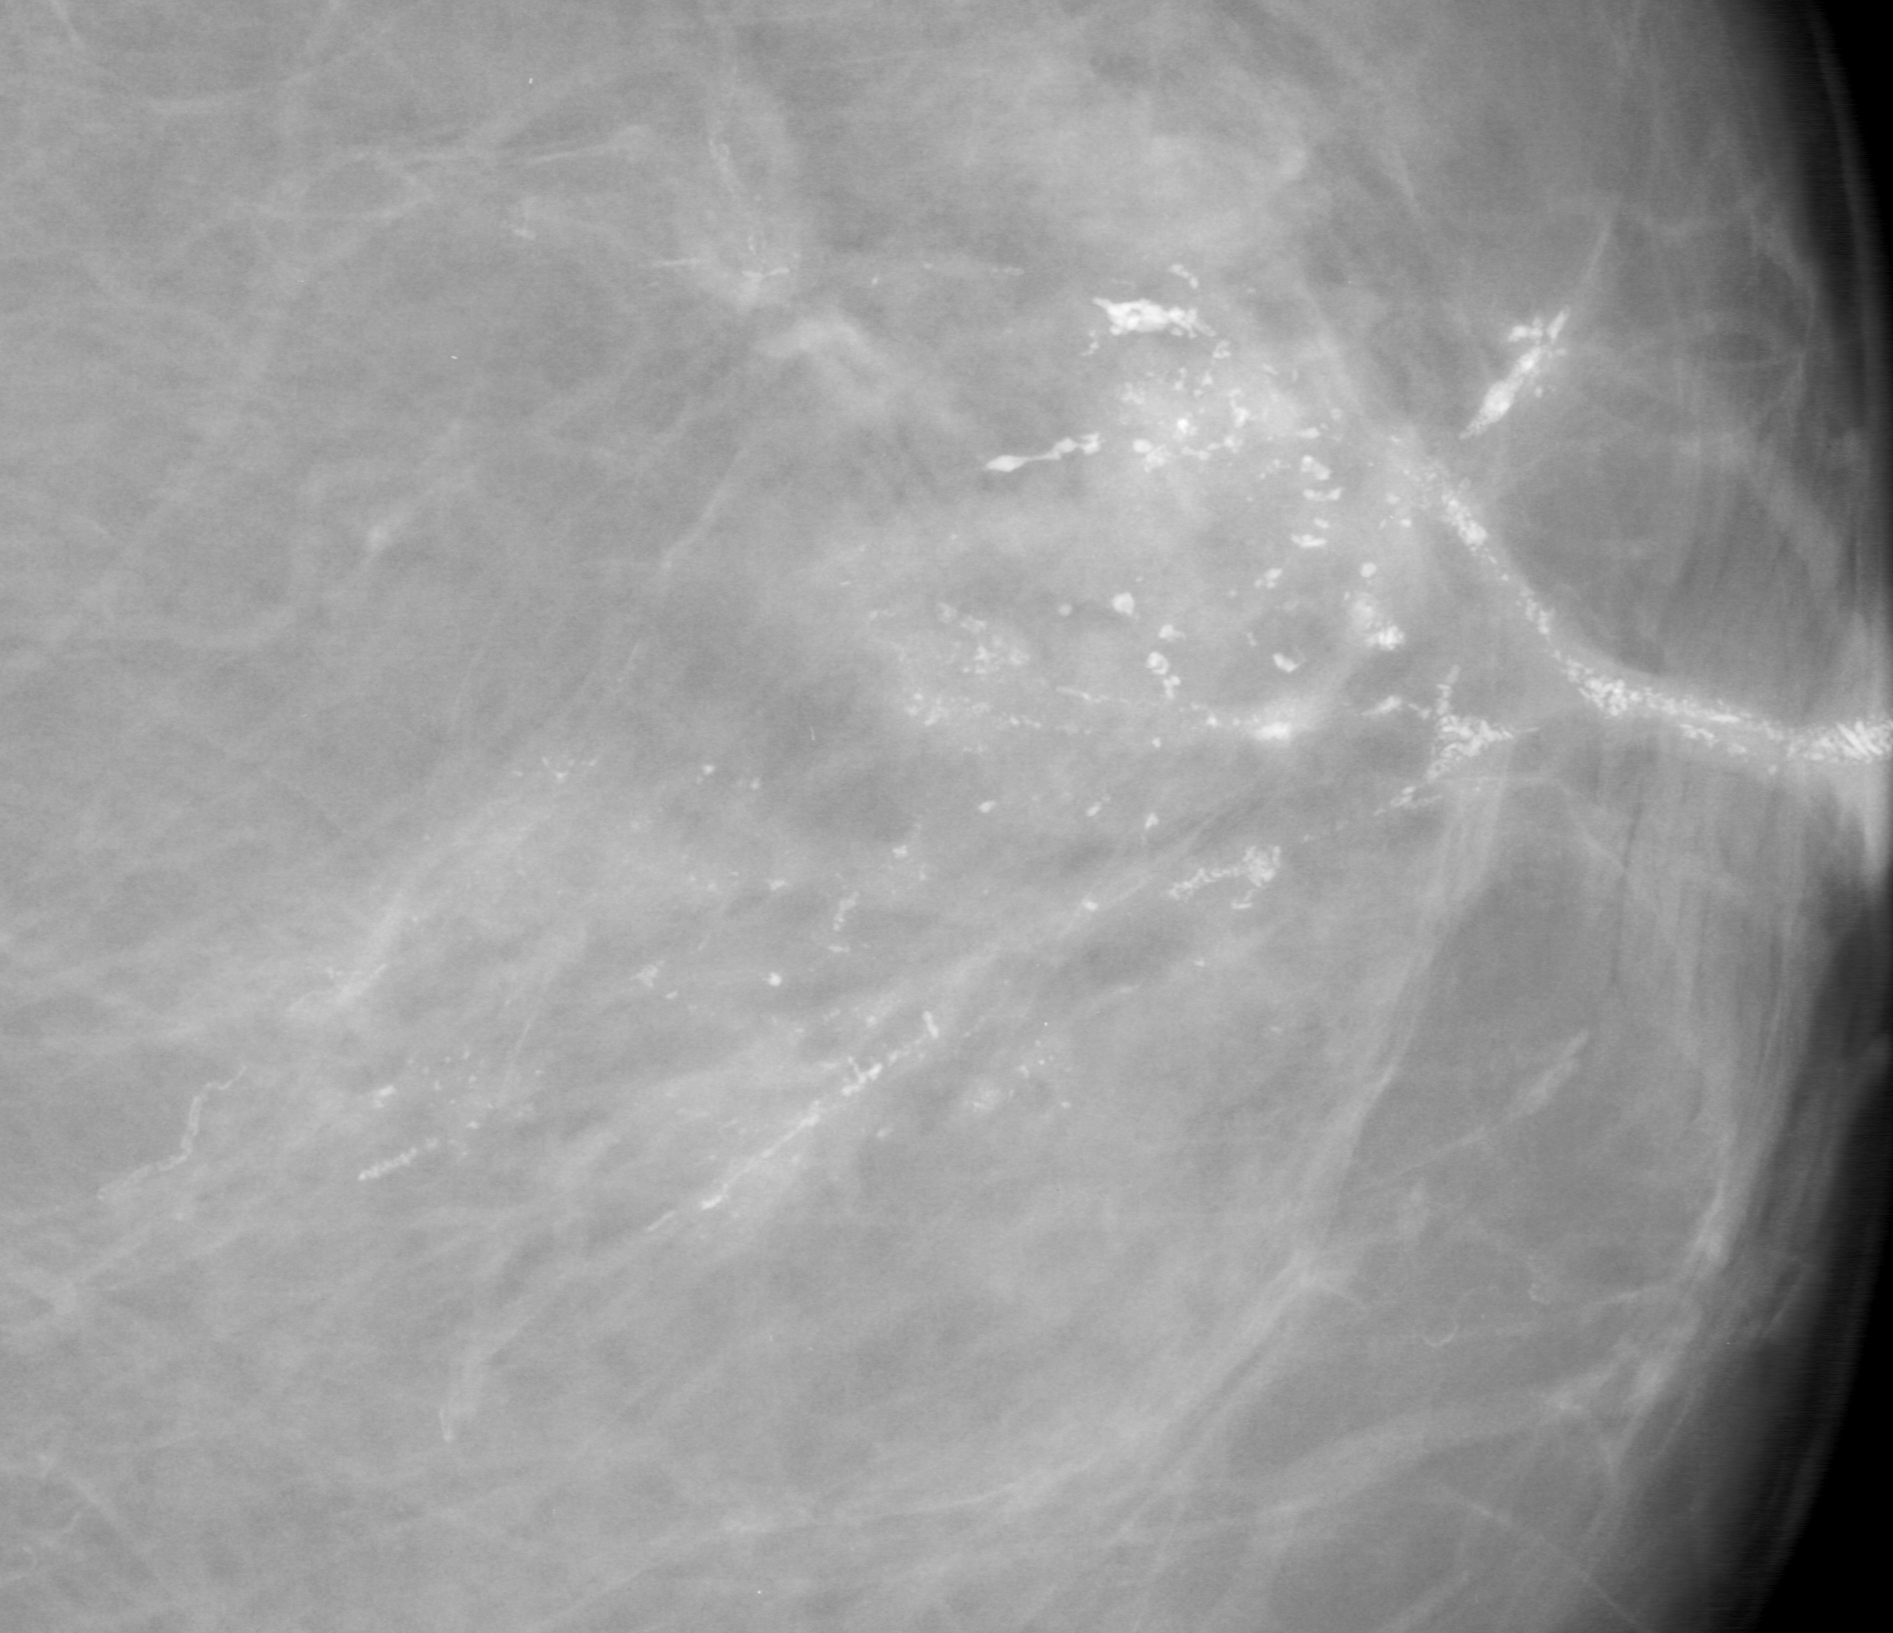
Cropped region of a digitized screen-film mammogram centred on a radiologist-marked abnormality; left breast; CC view; BI-RADS breast density category 1 (scale 1–4).
Calcifications, morphology pleomorphic, distribution linear; BI-RADS assessment category 5; subtlety rating 5 on a 1 (subtle) to 5 (obvious) scale; pathology result (as recorded, not read from the image): malignant.